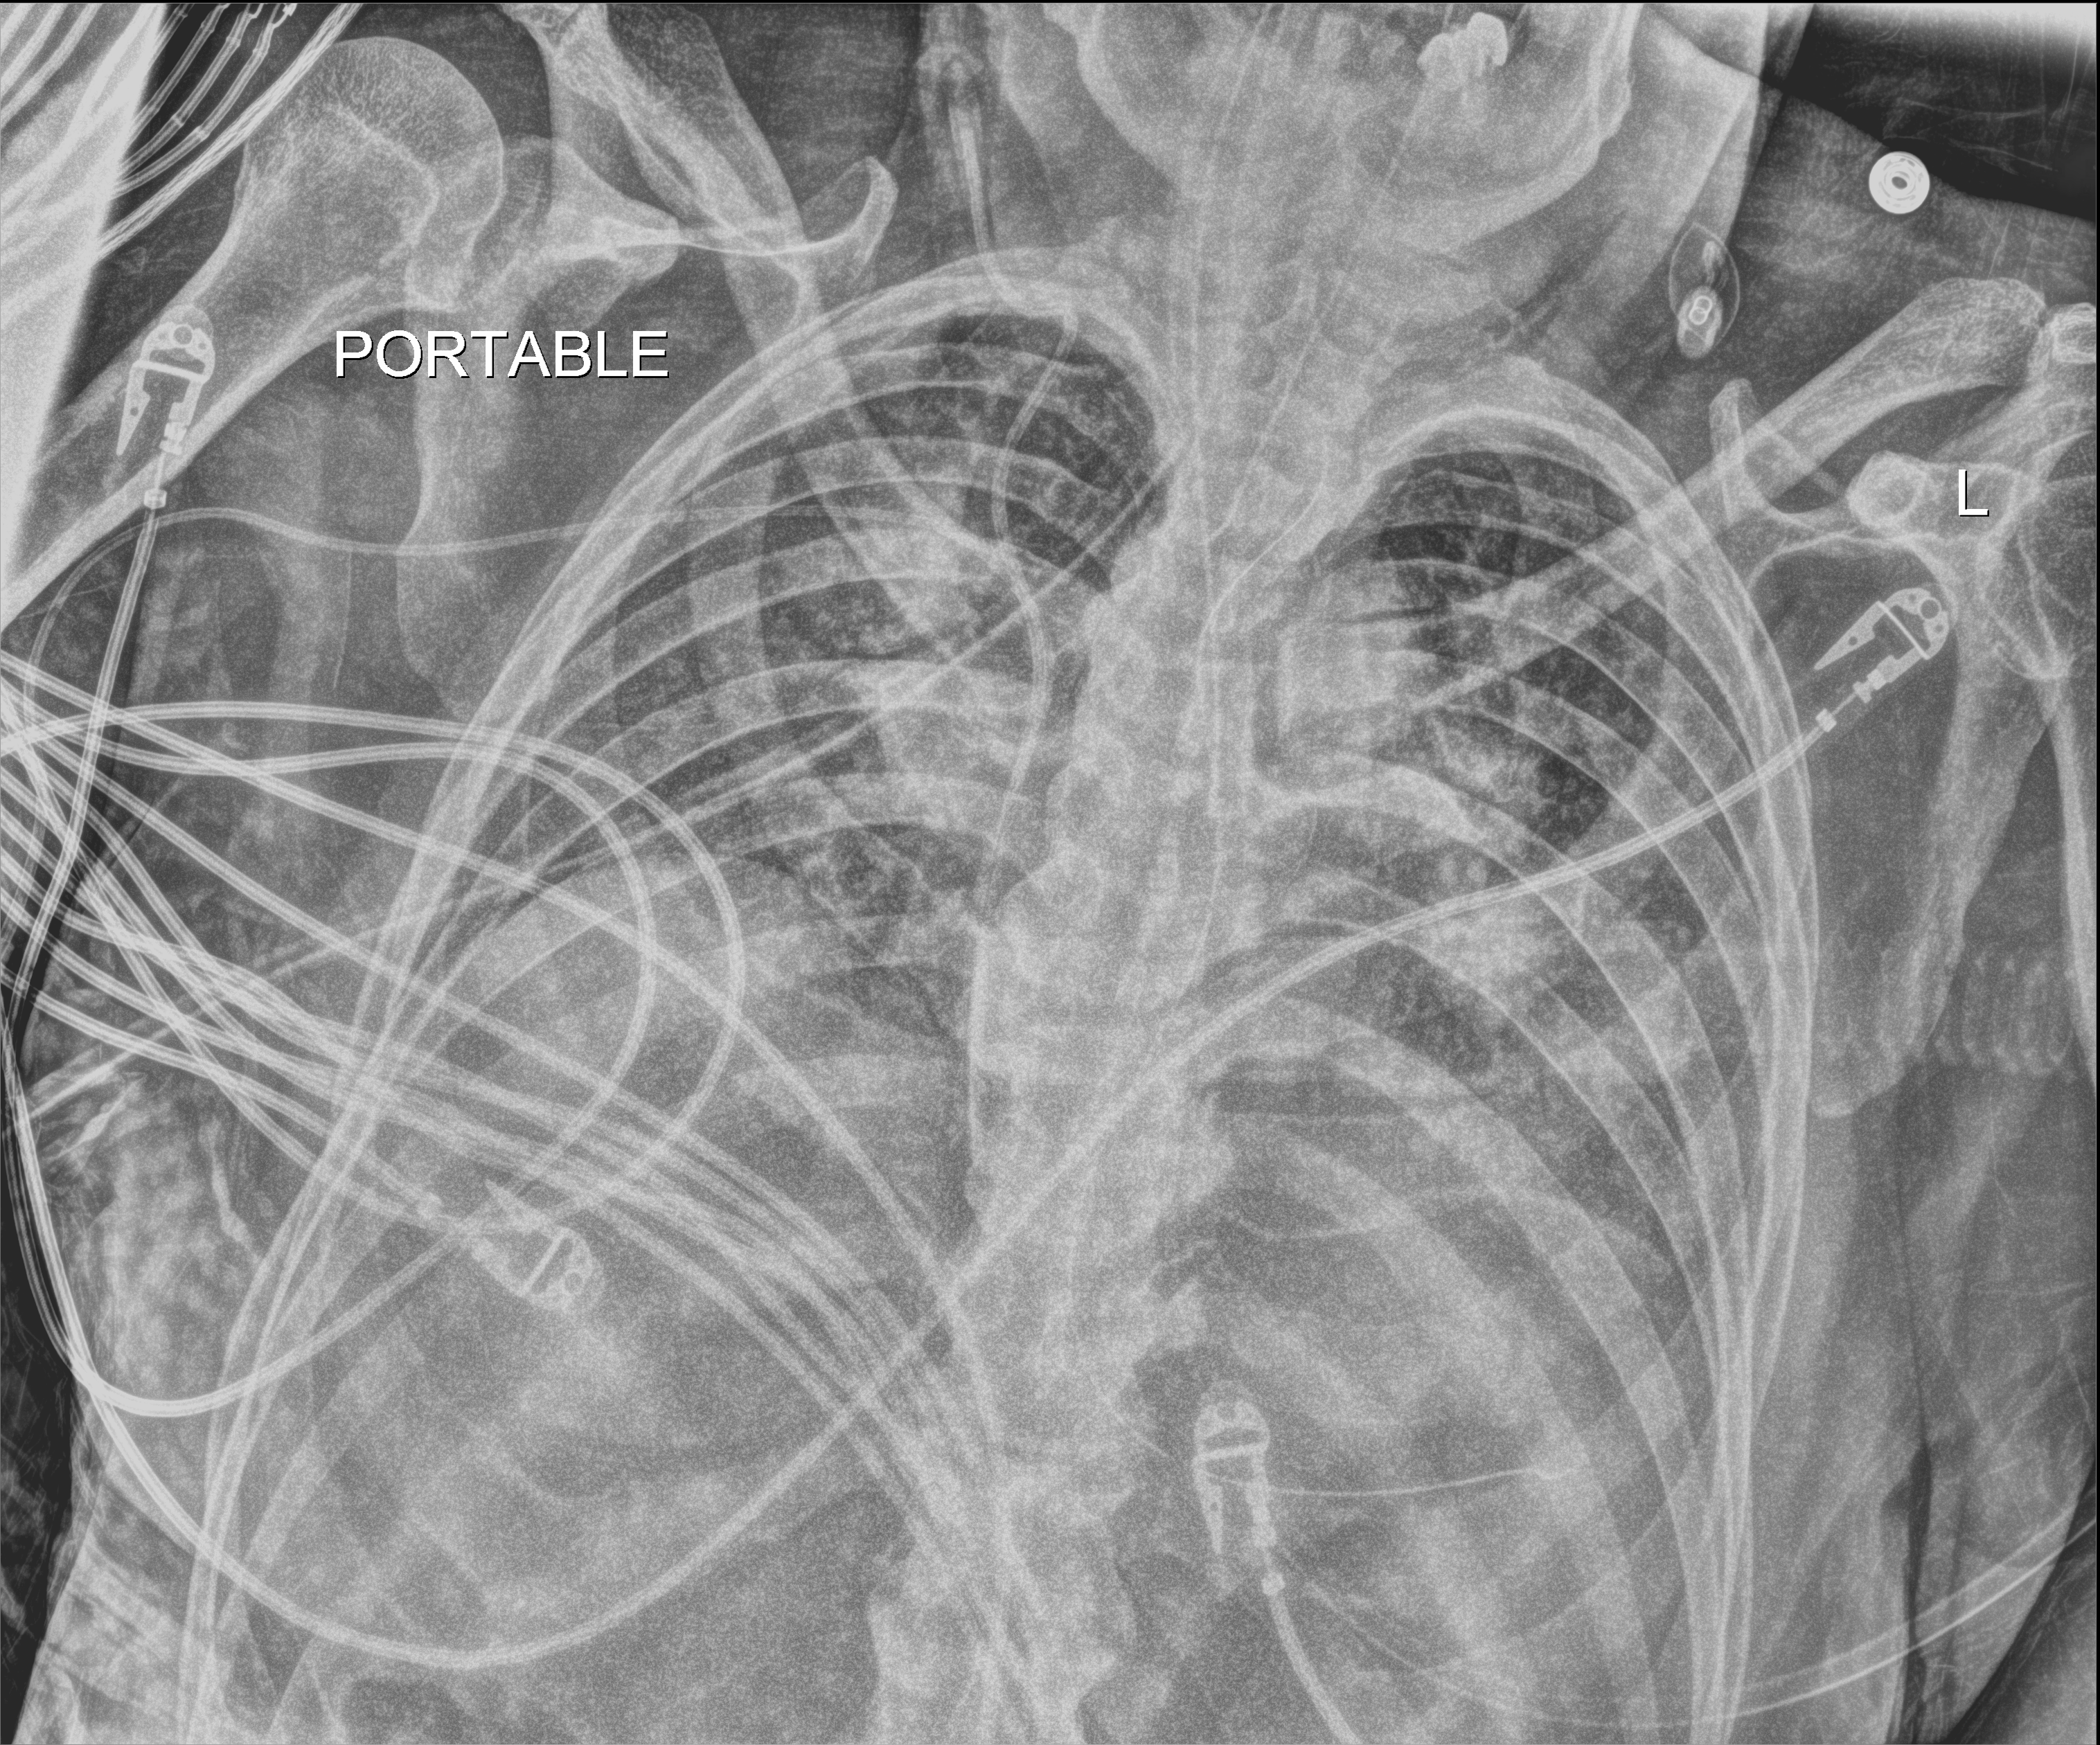
Chest X-ray (portable). Male patient hospitalised with COVID-19, age 75–90 years.
From the hospital-stay record, not from the radiograph (when in the stay this image was taken is not recorded): admitted to intensive care during this hospital stay: yes; hypertension (admission record): yes.